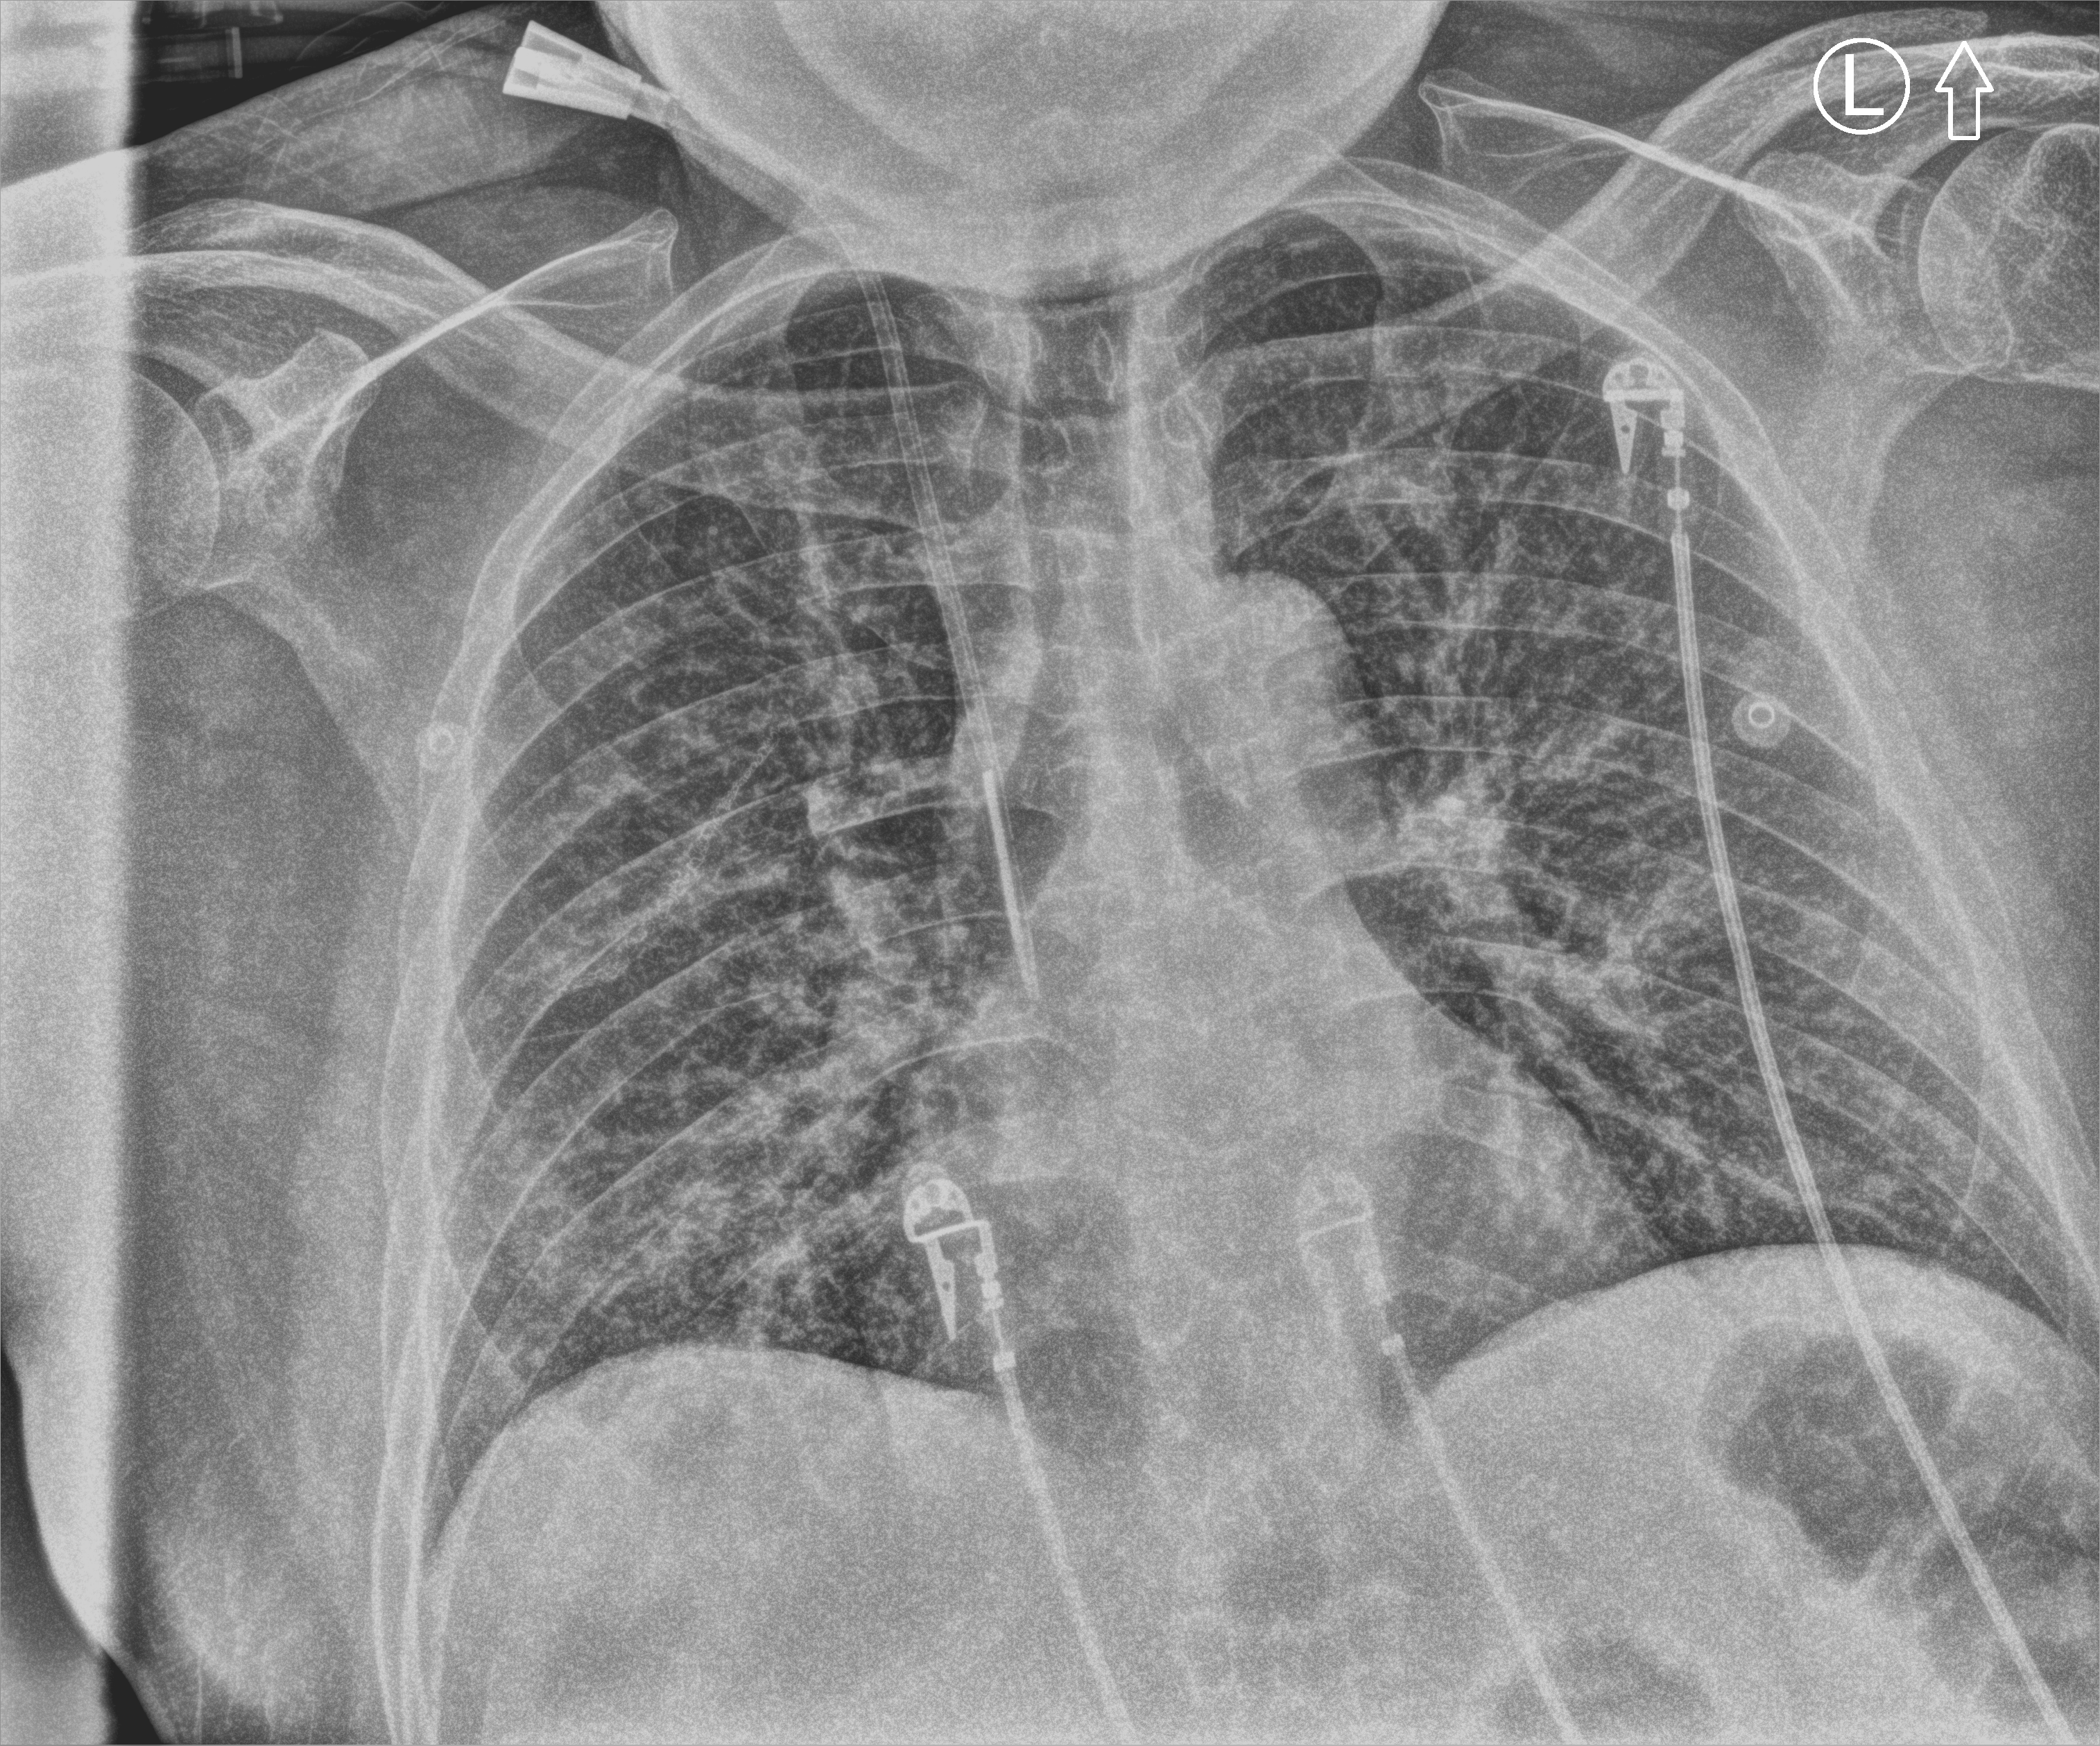
Portable chest radiograph; anteroposterior (AP) projection. Patient hospitalised with COVID-19; male, aged 18–59 years.
From the hospital-stay record, not from the radiograph (when in the stay this image was taken is not recorded): COPD (admission record): no; mechanically ventilated during this hospital stay: no.